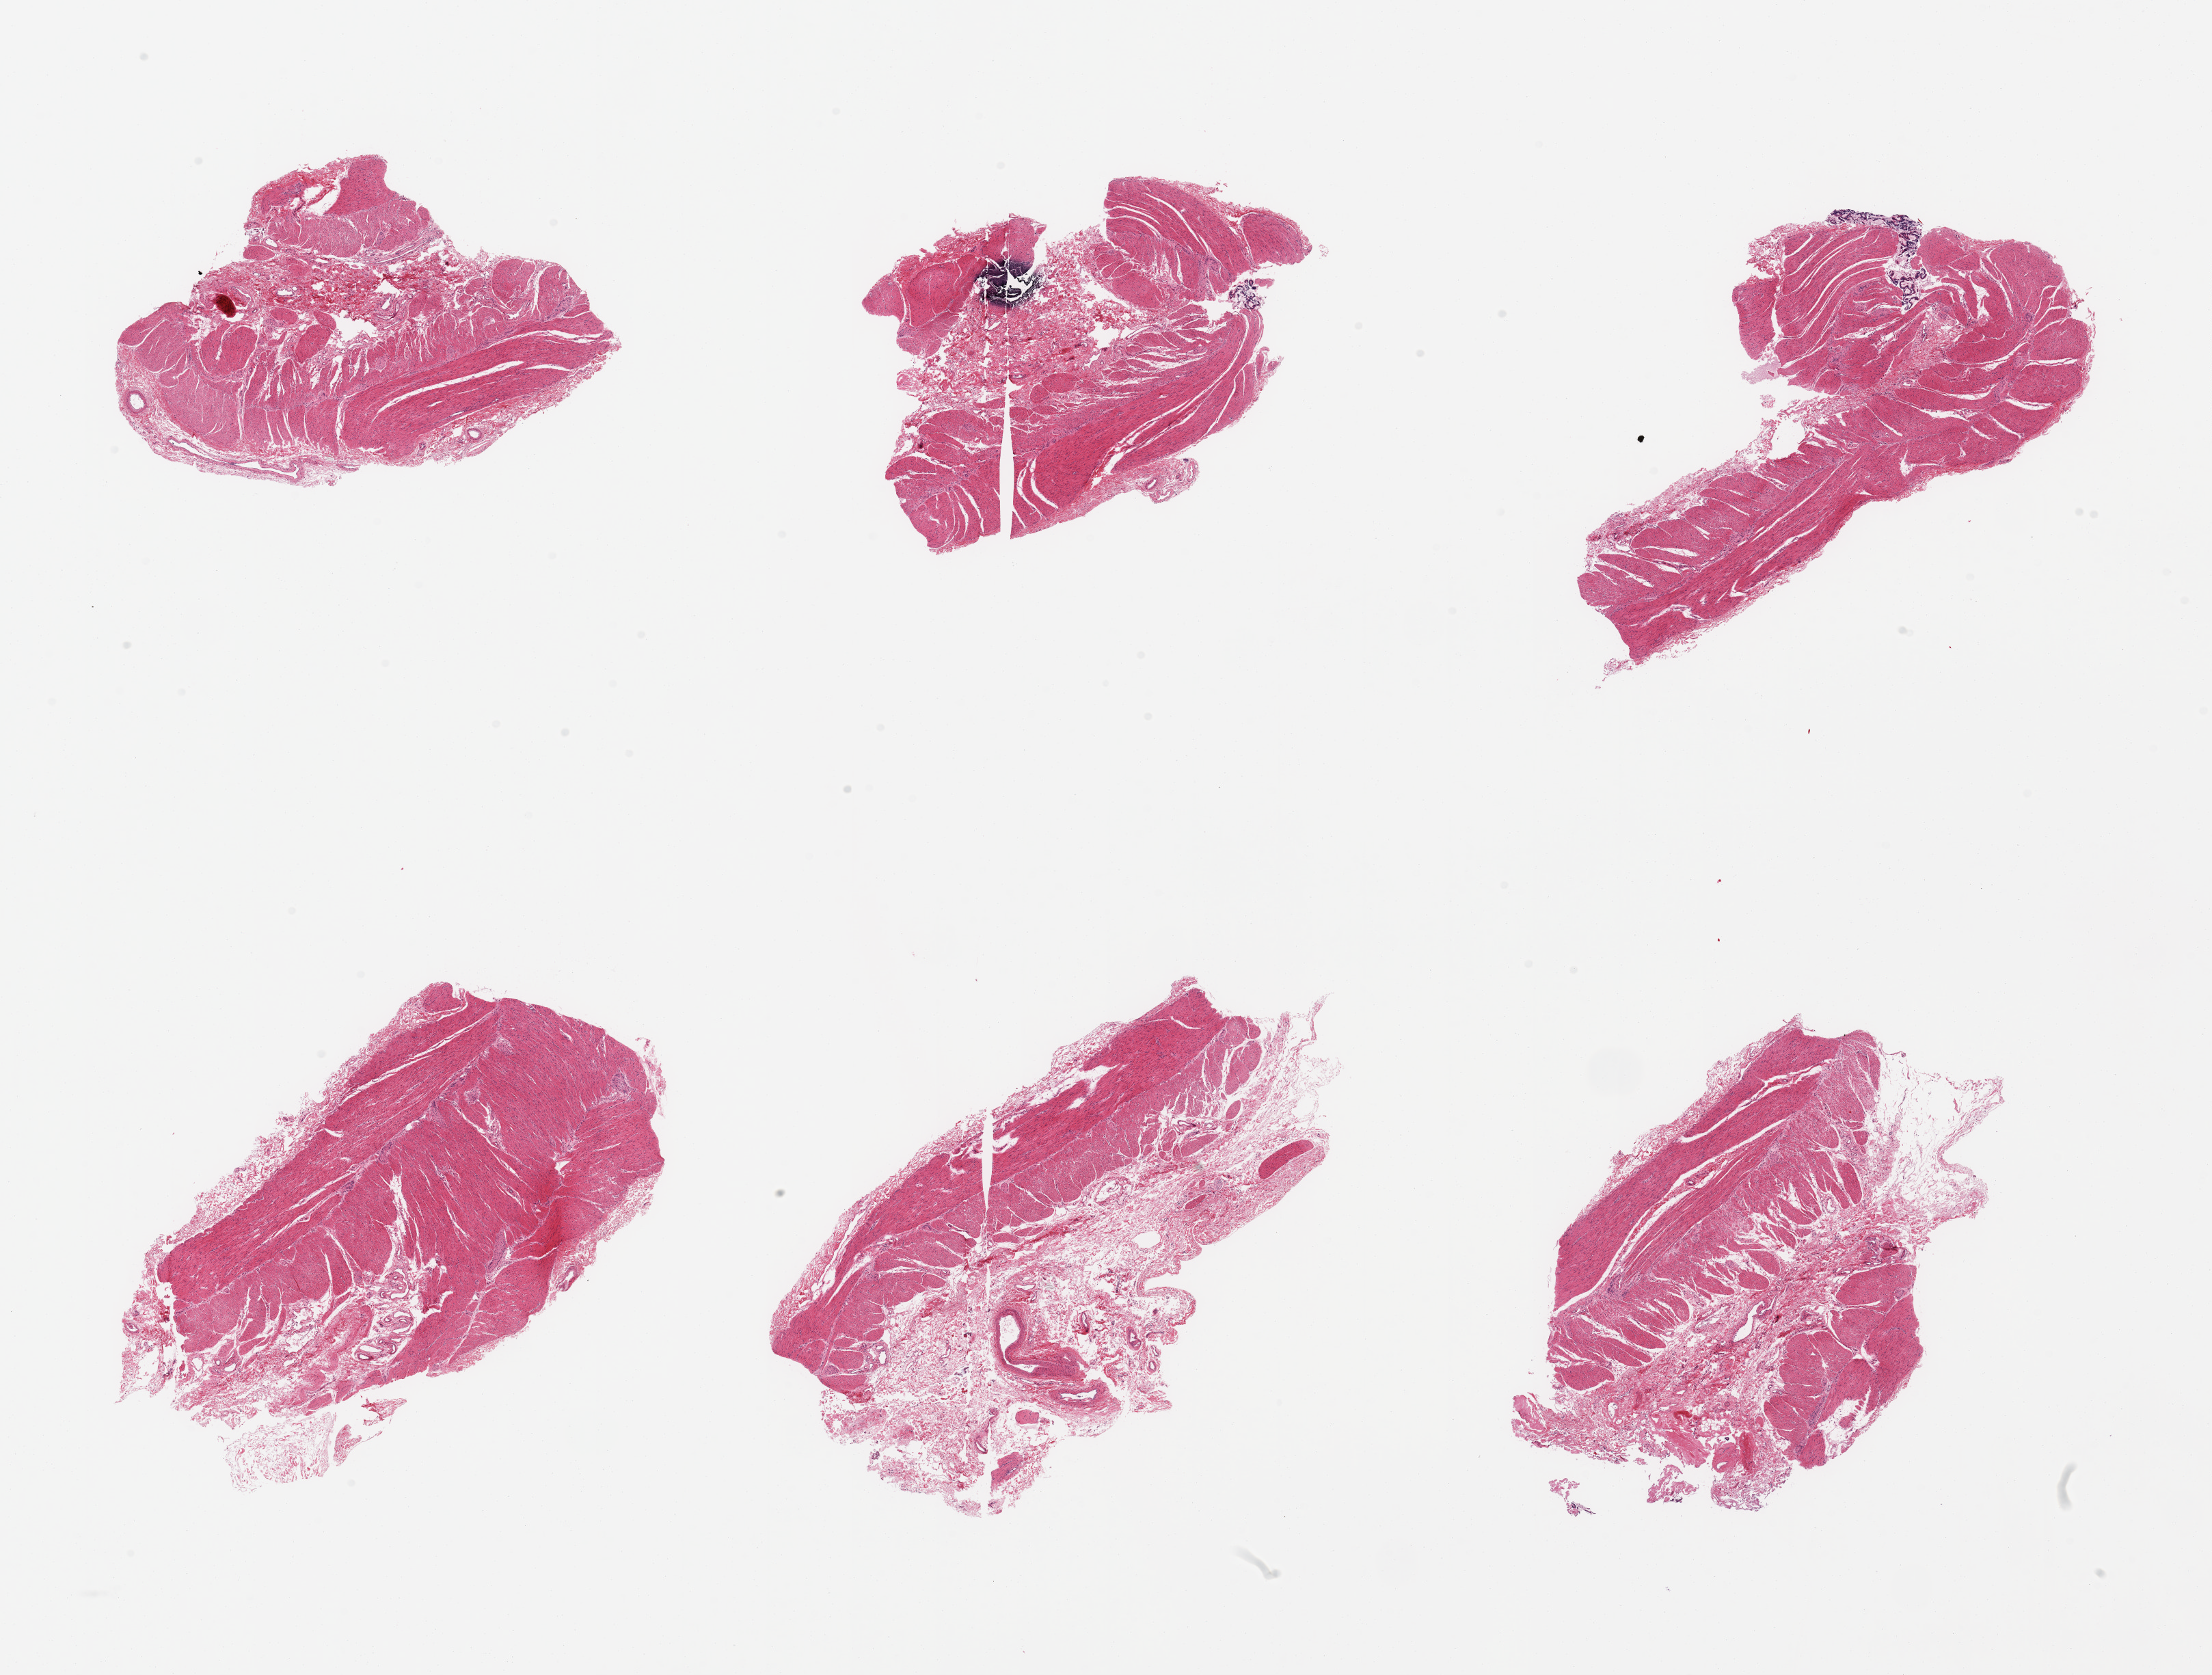
Whole-slide image, H&E stain, brightfield, shown as a low-resolution overview of the whole scanned area (about 25.6 x 19.4 mm, slide scanned at 20x); PAXgene-fixed paraffin-embedded (PFPE) section; sampled site (target tissue): ileum; donor tissue sample. Donor sex: female.
Review note (as recorded): 6 pieces; all have muscularis, no lymphoid tissue.